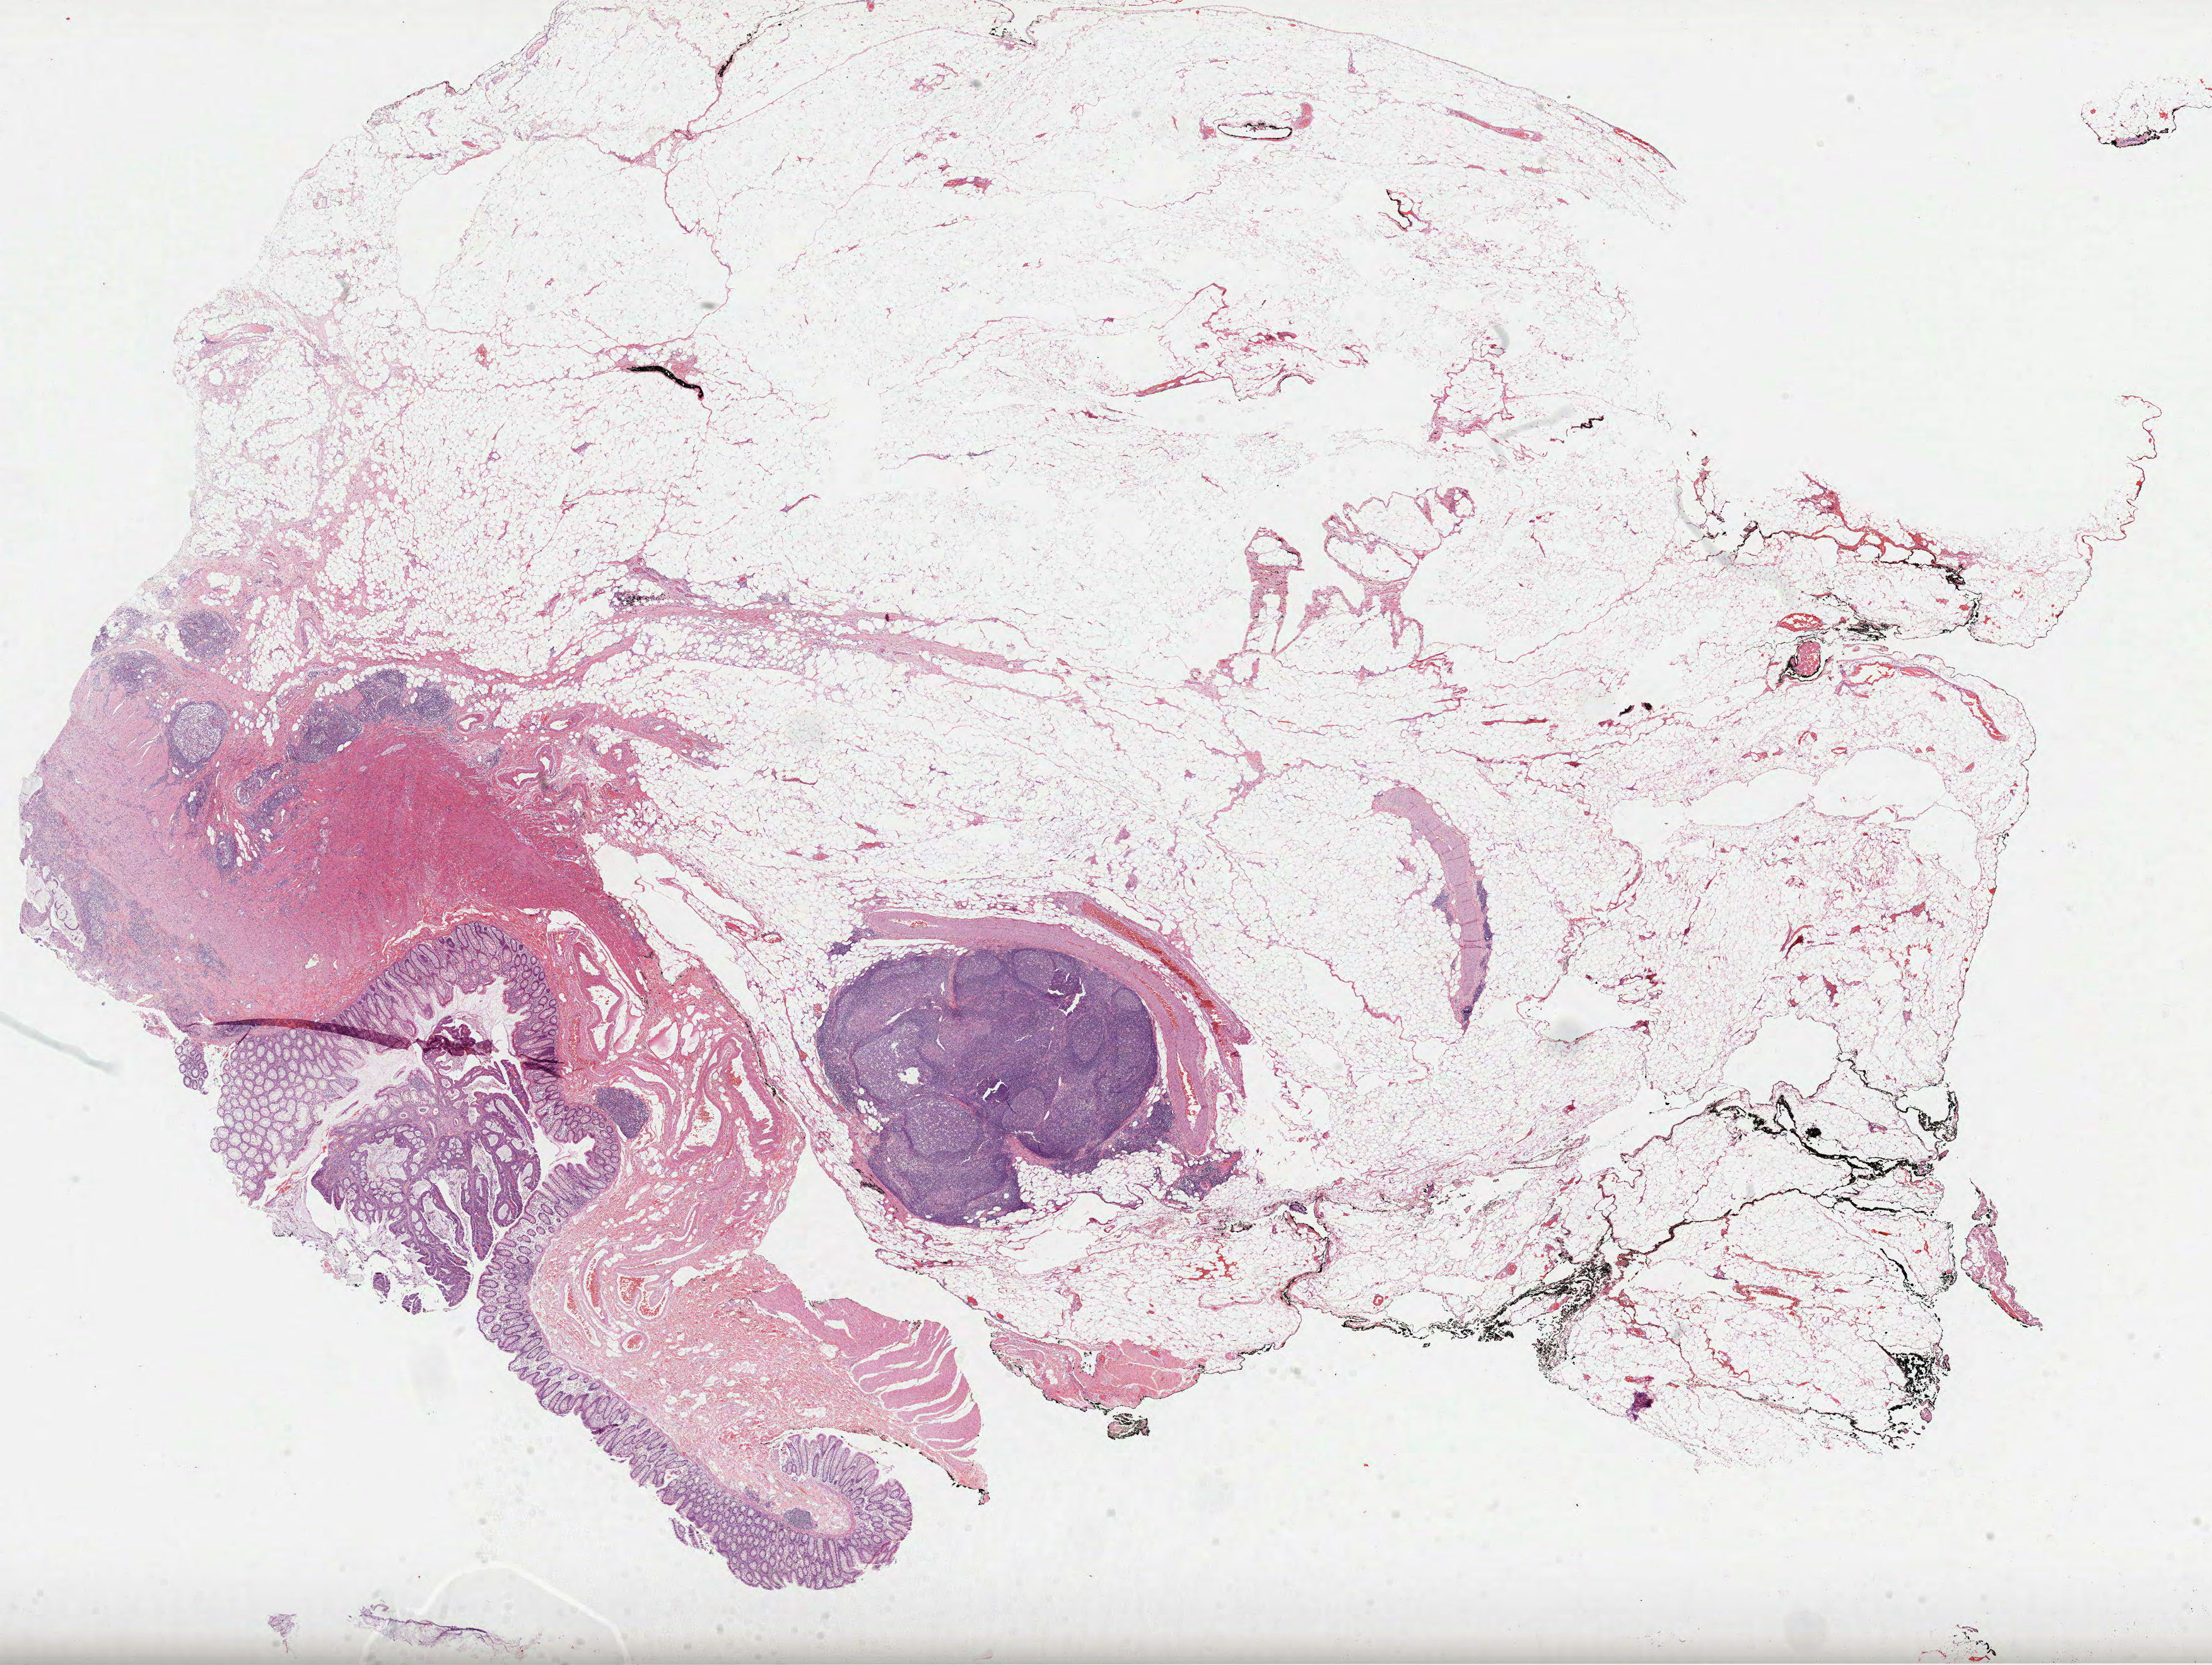
H&E-stained whole-slide image — a low-resolution overview of the entire scanned area, about 28.3 x 21.3 mm (from a 40x scan), formalin-fixed paraffin-embedded (FFPE) diagnostic section, colon, primary tumour sample. Patient: female, age at initial diagnosis 60 years.
Lymph nodes positive (case pathology): 3 of 44 examined. AJCC pathologic stage: III. Histologic diagnosis: Adenocarcinoma, NOS (cecum).